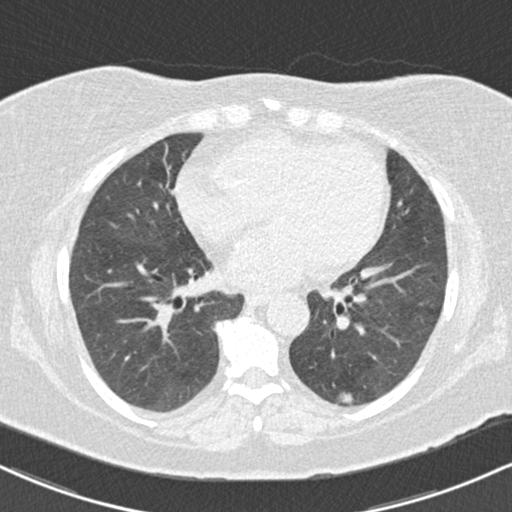
Low-dose screening chest CT, one axial slice. Slice 69 of 147 in the series (ordered by position). 120 kVp. Lung window (W 1500 / L -600 HU). 2 mm slice thickness. 512 × 512 image matrix.
Outlined on this slice (manually delineated by an expert):
- lesion 1 (tumor, lower lobe of left lung): bounding box <339,393,353,404> (left, top, right, bottom; pixels)